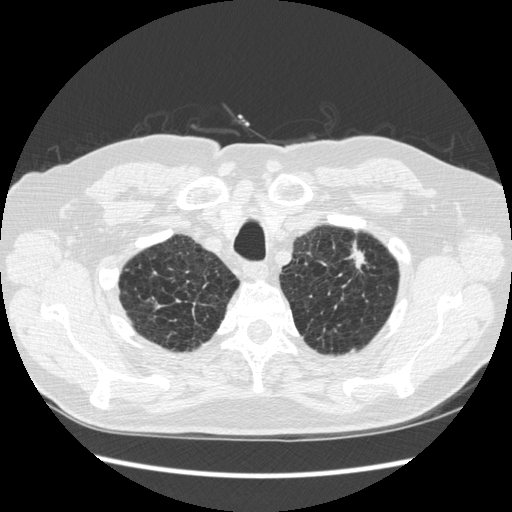
Low-dose screening chest CT, axial slice; third annual screen; lung window (W 1500 / L -600 HU); 1.25 mm slice thickness; standard (soft-tissue) reconstruction kernel (STANDARD); slice 32 of 267 in the series; 512 × 512 image matrix, field of view 360 × 360 mm. Male participant, aged 70 years at enrolment.
- Lesion marked by an expert reader, bounding box (x1, y1, x2, y2) in pixels: (324, 232, 379, 297).
- The screening reader recorded 2 non-calcified nodules or masses ≥4 mm on this exam; which of them this box marks is not recorded.
- Participant outcome: lung cancer diagnosed 92 days after this screen — squamous cell carcinoma, NOS, left upper lobe, moderately differentiated (G2), stage IA (AJCC 6th edition), 18 mm at pathology.